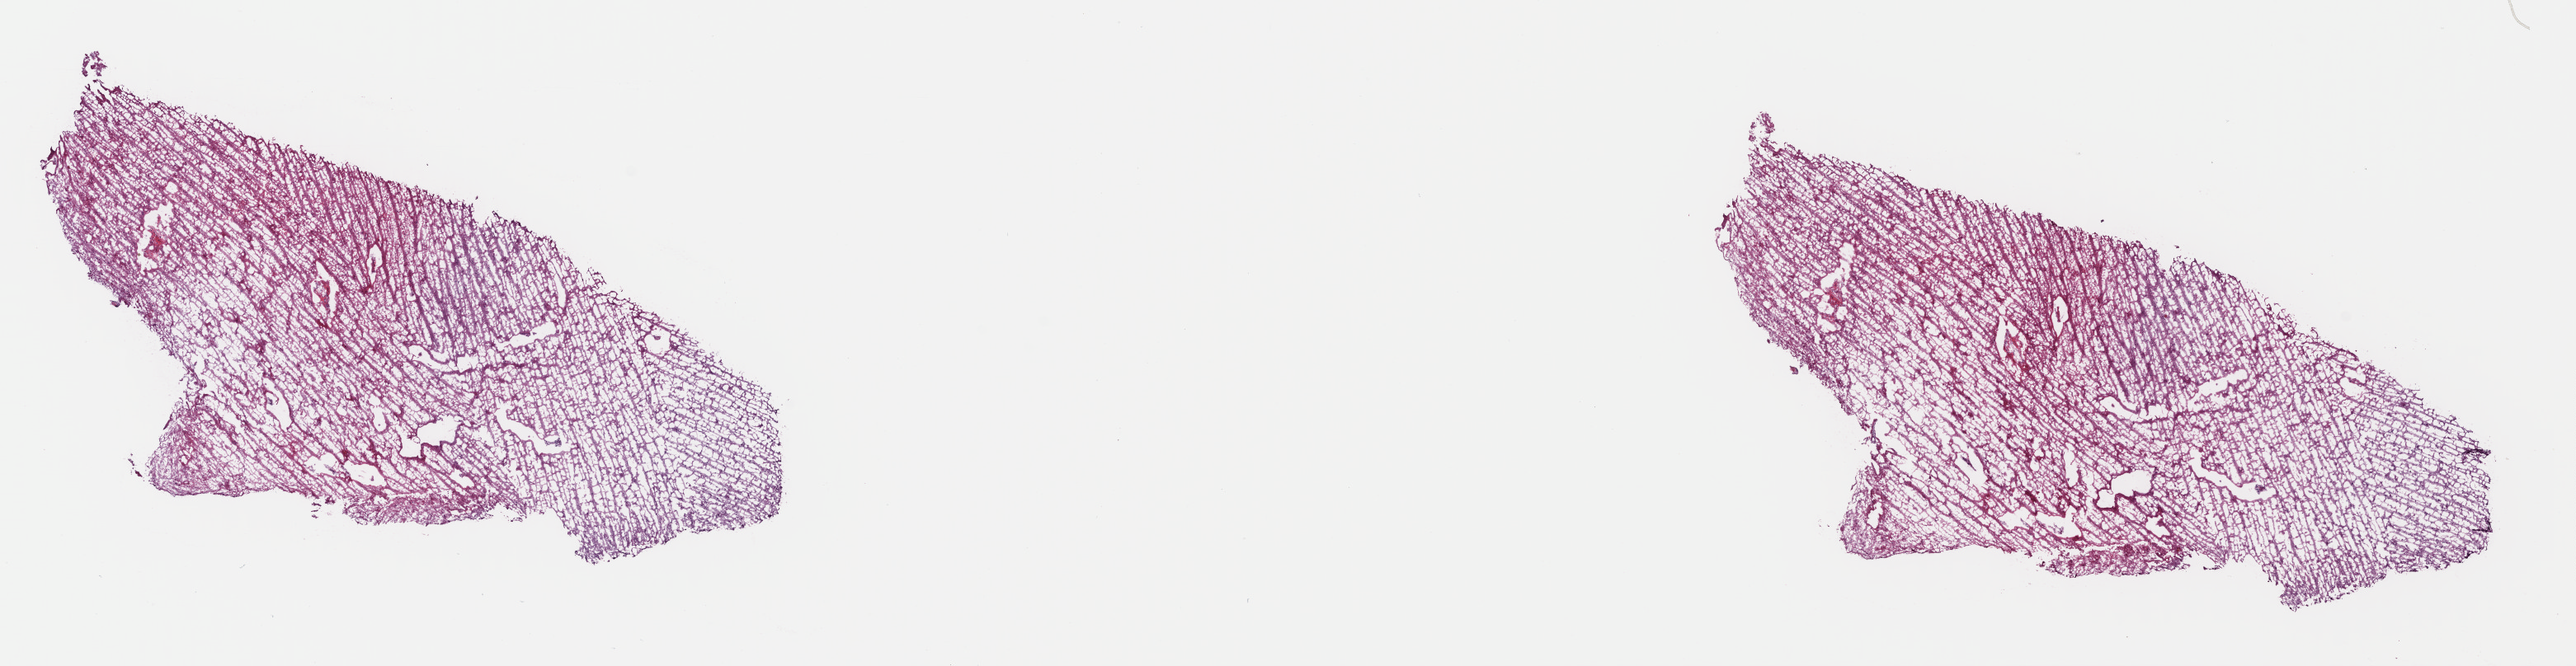
H&E whole-slide image, shown as a low-resolution overview of the whole scanned area (about 24.6 x 6.4 mm, from a 40x scan). Frozen section from the top of the tissue portion. Brain, primary tumour sample. Female patient; age at initial diagnosis 44 years. Histologic grade: G3 (poorly differentiated). Pathologist review of this section (percent, as recorded): tumour cells 30%, tumour nuclei 70%, normal cells 10%, stromal cells 60%, necrosis 0%. Inflammatory infiltration, as recorded: lymphocyte infiltration 0%, monocyte infiltration 0%, neutrophil infiltration 0%.
• histologic diagnosis: Astrocytoma, anaplastic (cerebrum)